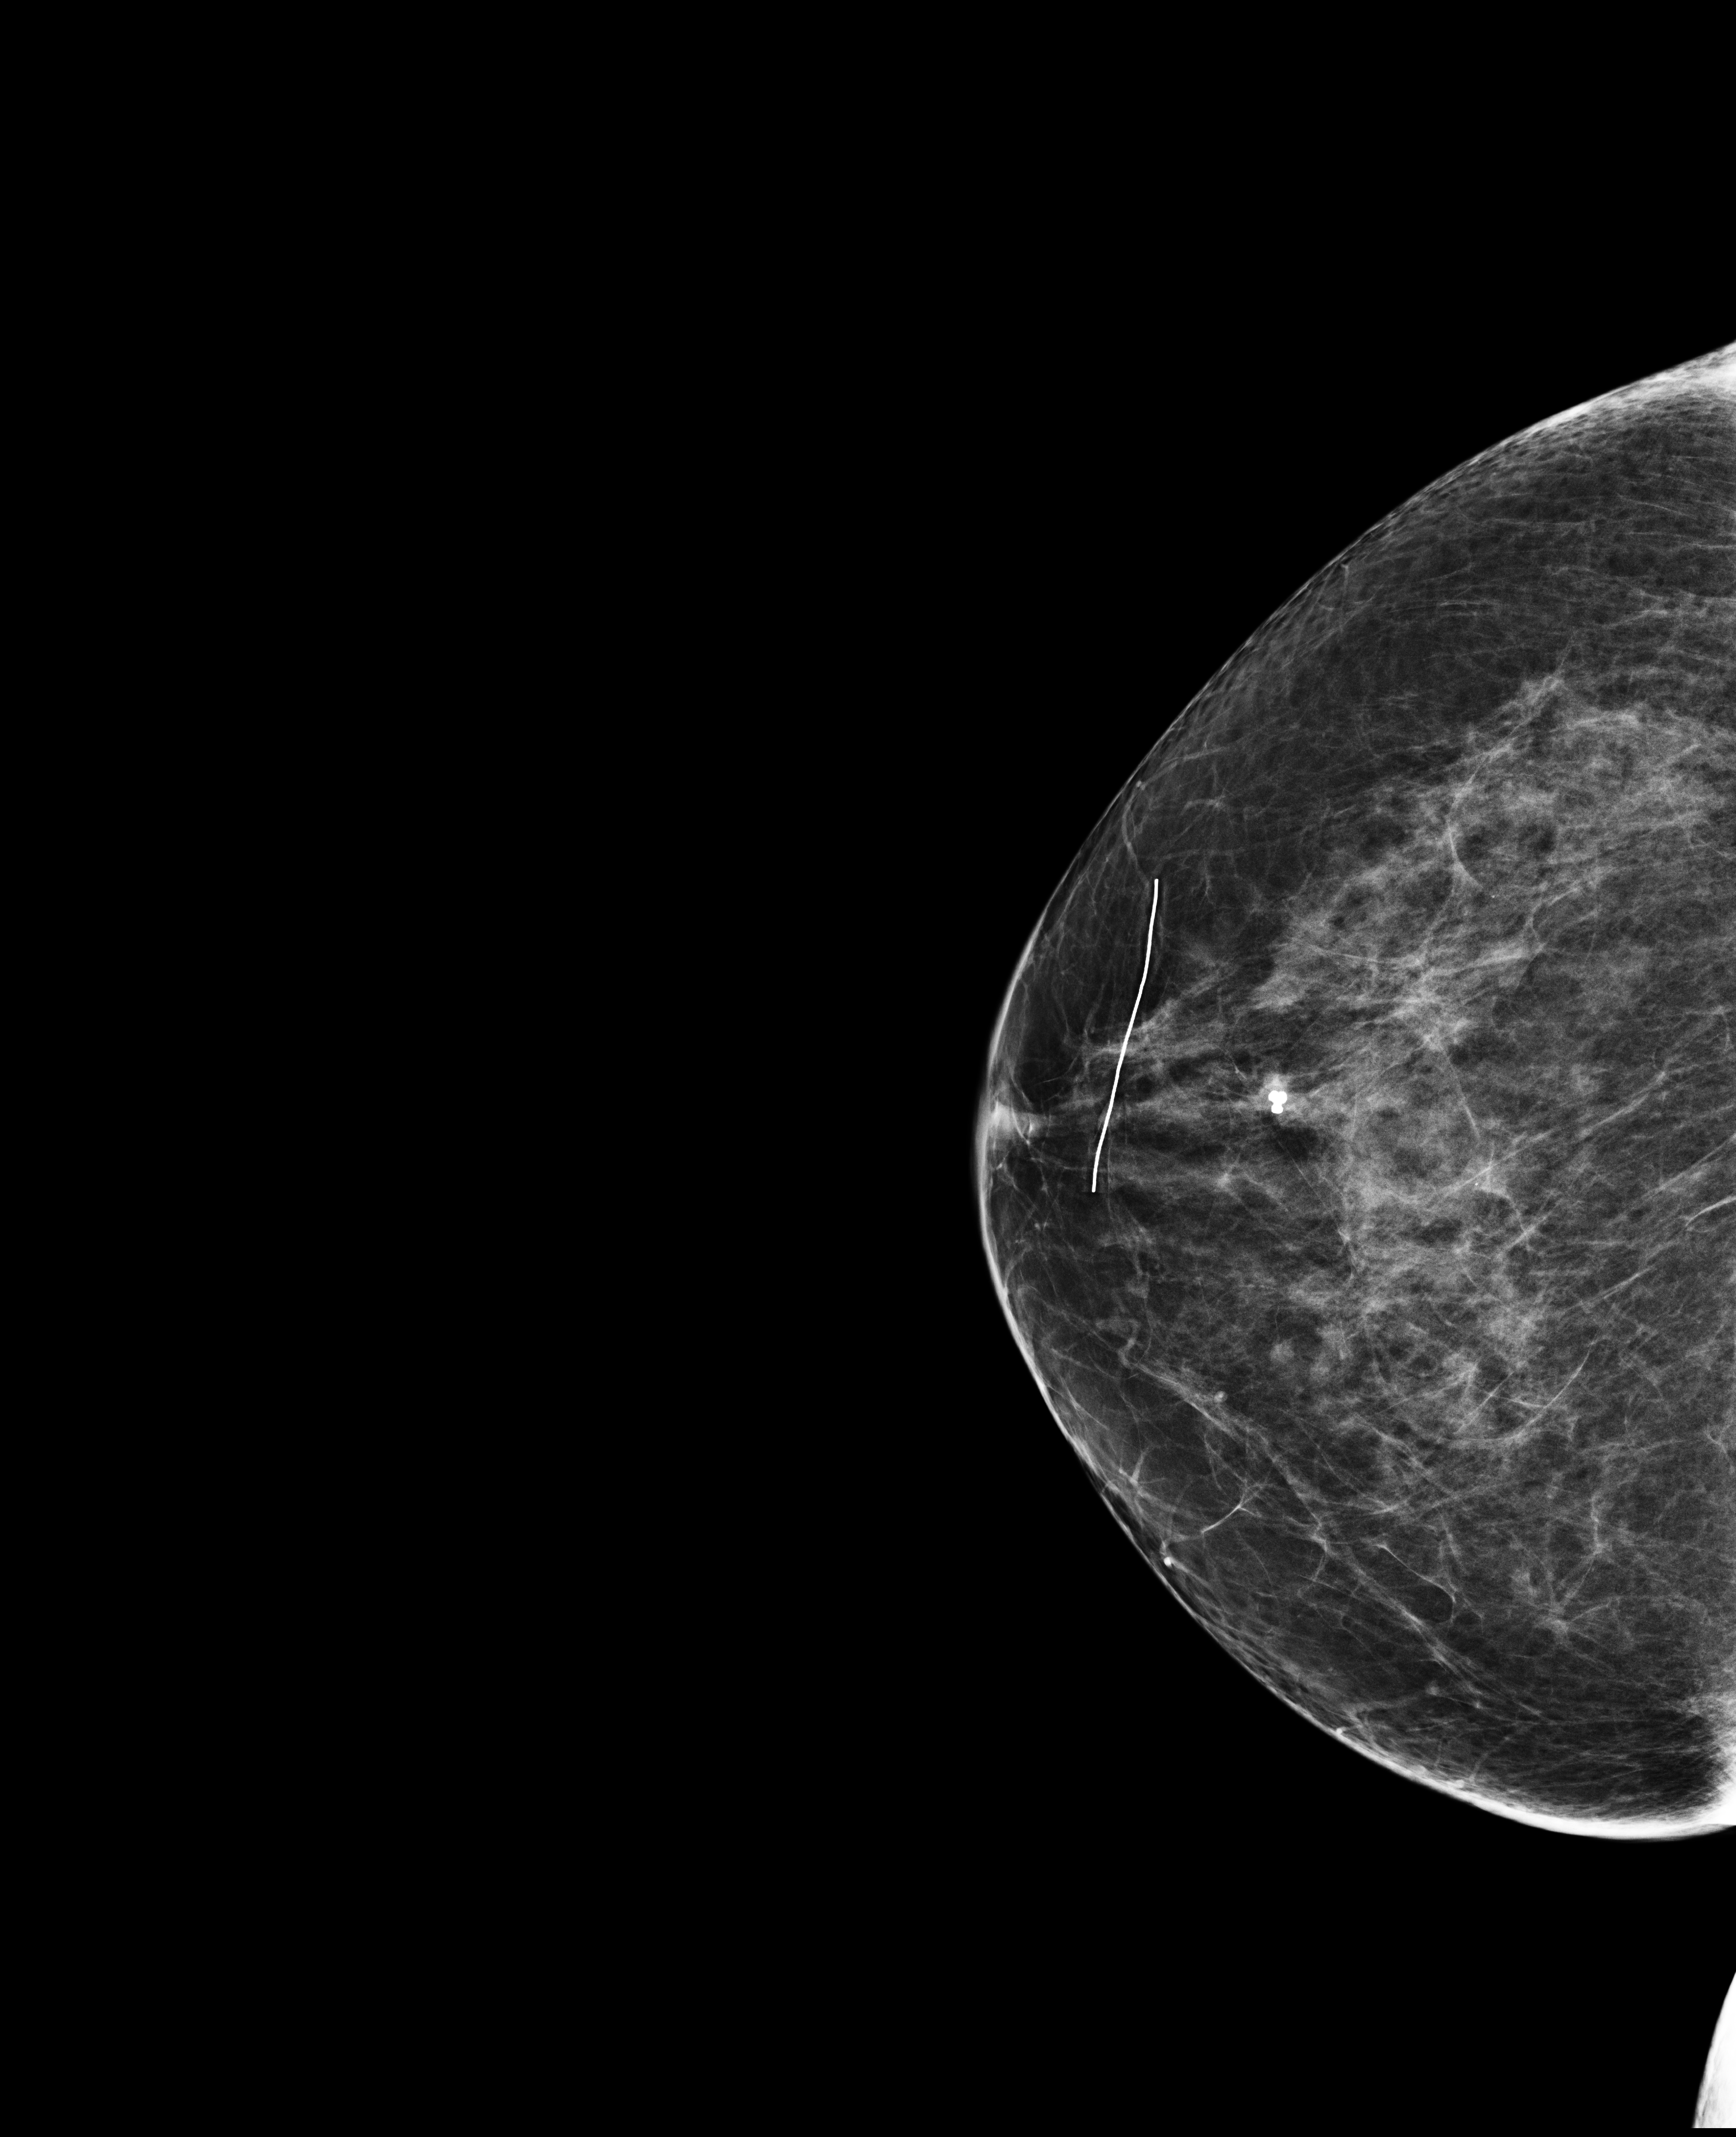
Annual screening mammography examination, compressed breast thickness 58 mm. Patient aged 68 years (female).
Image type: full-field digital mammogram. Breast: right. Projection: CC view.